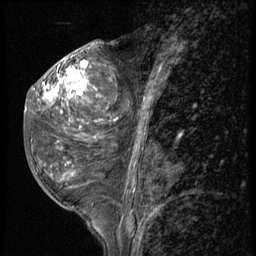
Breast MRI (dynamic contrast-enhanced), one sagittal slice. Position 24 of 56 along the scan axis. 3 images stored at this slice position (order not interpretable as contrast timing). 1.5 T. TE 4.2 ms, TR 9 ms. 2.5 mm slice thickness. 256 × 256 image matrix. Patient: female, 50 years. Case-level facts recorded for this patient, not image findings: setting: breast cancer imaged before/during neoadjuvant chemotherapy; receptor status: triple-negative.
Annotated regions visible in this slice (semi-automatically segmented with operator editing):
- analysis volume of interest (the breast-tissue region the enhancement analysis was run in; not a lesion): bounding box (x1, y1, x2, y2) in pixels: (25, 50, 117, 191)
- tumour enhancement mask (voxels above the 140 % enhancement threshold inside the analysis volume of interest): (43, 61, 88, 101)